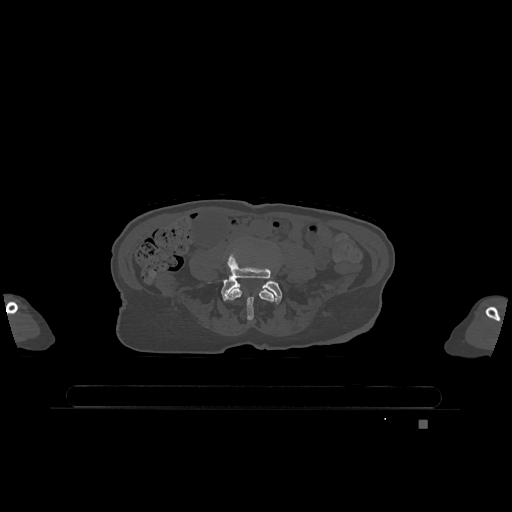
CT including the spine, one axial slice. Position 265 of 1317 along the scan axis. Bone window (W 1800 / L 400 HU). 0.5 mm slice thickness. 512 × 512 image matrix, field of view 500 × 500 mm. Female patient, age 74 years. Case-level facts recorded for this patient, not image findings: primary cancer: lung.
Annotated regions visible in this slice (semi-automatically segmented with operator editing):
- L4 vertebra: box from (x=228, y=289) to (x=274, y=321) px
- L5 vertebra: (x=221, y=257)–(x=282, y=304)